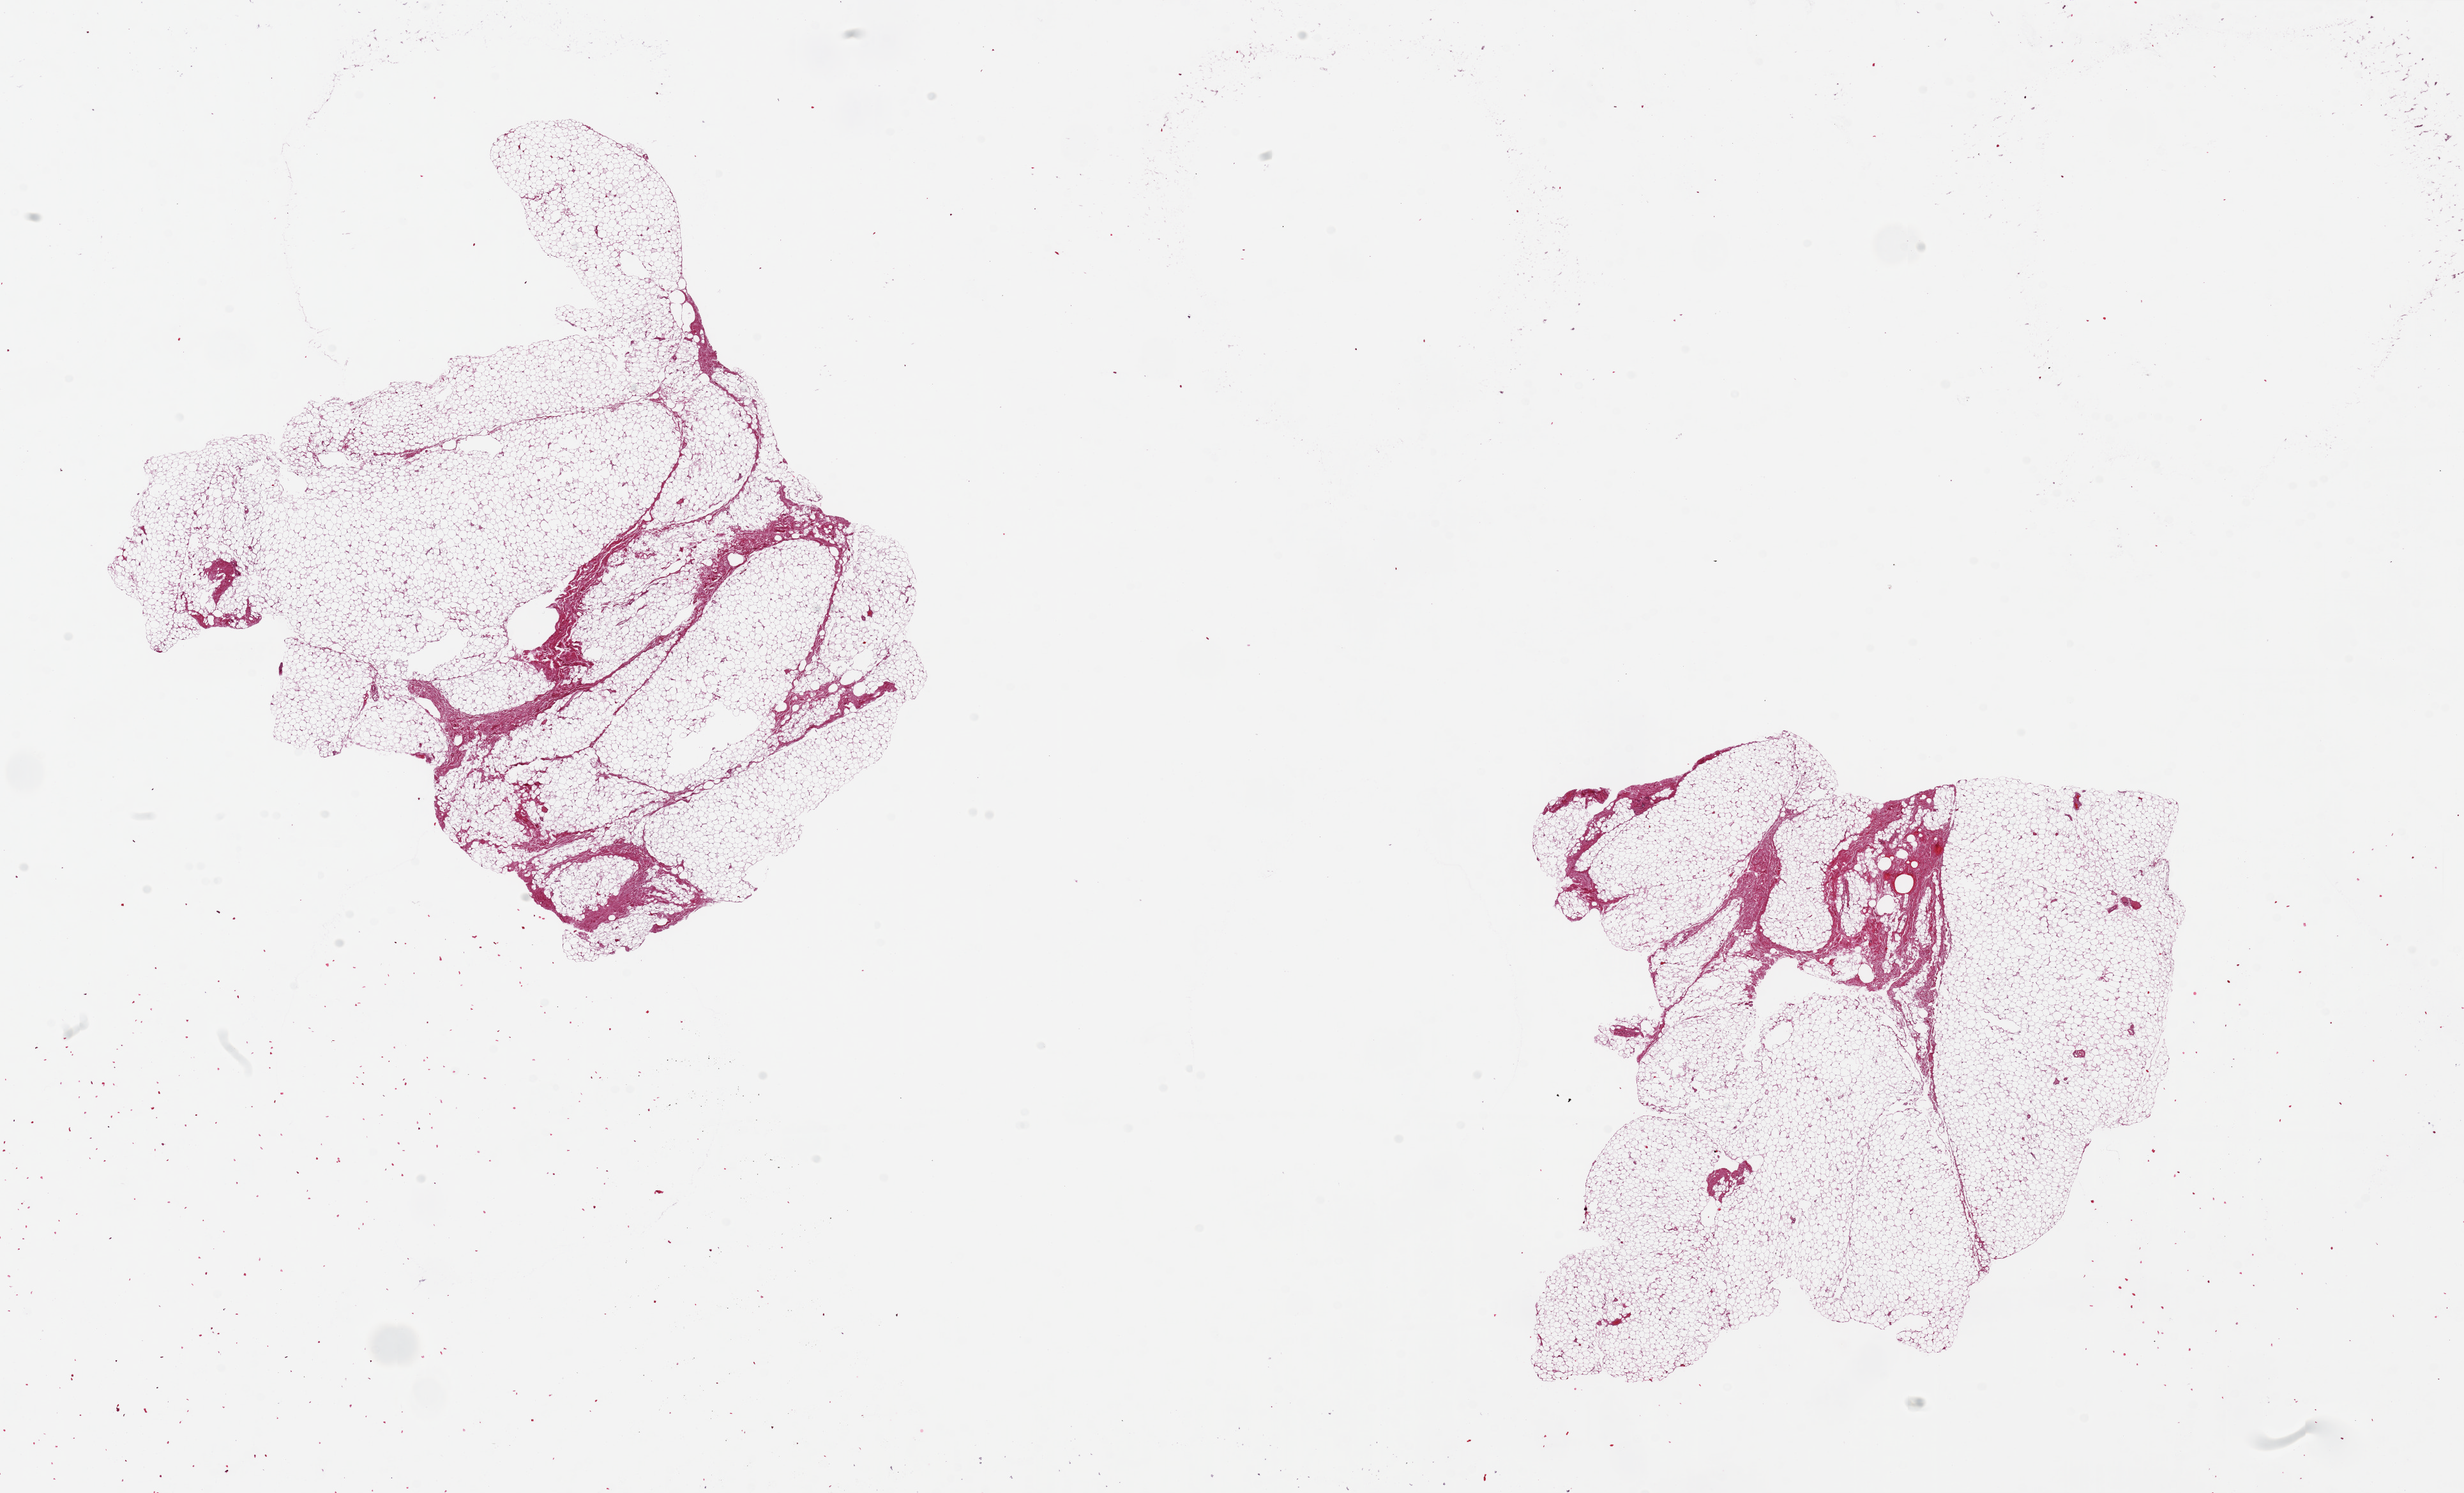
Whole-slide image, haematoxylin and eosin stain, brightfield, shown as a low-resolution overview of the whole scanned area (about 30.5 x 18.5 mm), PAXgene-fixed, paraffin-embedded tissue, sampled site (target tissue): breast, tissue donor sample. Donor: male.
Pathologist's review note for this sample: 2 pieces ~9x8mm, all fibroadipose tissue; not ductal elements noted.